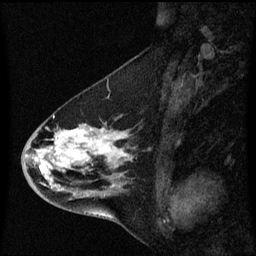
Breast MRI (dynamic contrast-enhanced), one sagittal slice; position 27 of 60 along the scan axis; dynamic contrast-enhanced series, image 2 of 3 at this slice position (ordered by acquisition); 1.5 T; TE 4.2 ms, TR 8.4 ms; 2 mm slice thickness; 256 × 256 image matrix. Female patient, age 46 years. From the clinical record (not read from this slice): setting: breast cancer imaged before/during neoadjuvant chemotherapy; receptor status: HER2-positive.
Annotated regions visible in this slice (semi-automatically segmented with operator editing):
- analysis volume of interest (the breast-tissue region the enhancement analysis was run in; not a lesion): box from (x=22, y=112) to (x=135, y=195) px
- tumour enhancement mask (voxels above the 70 % enhancement threshold inside the analysis volume of interest): (x=35, y=130)–(x=130, y=187)